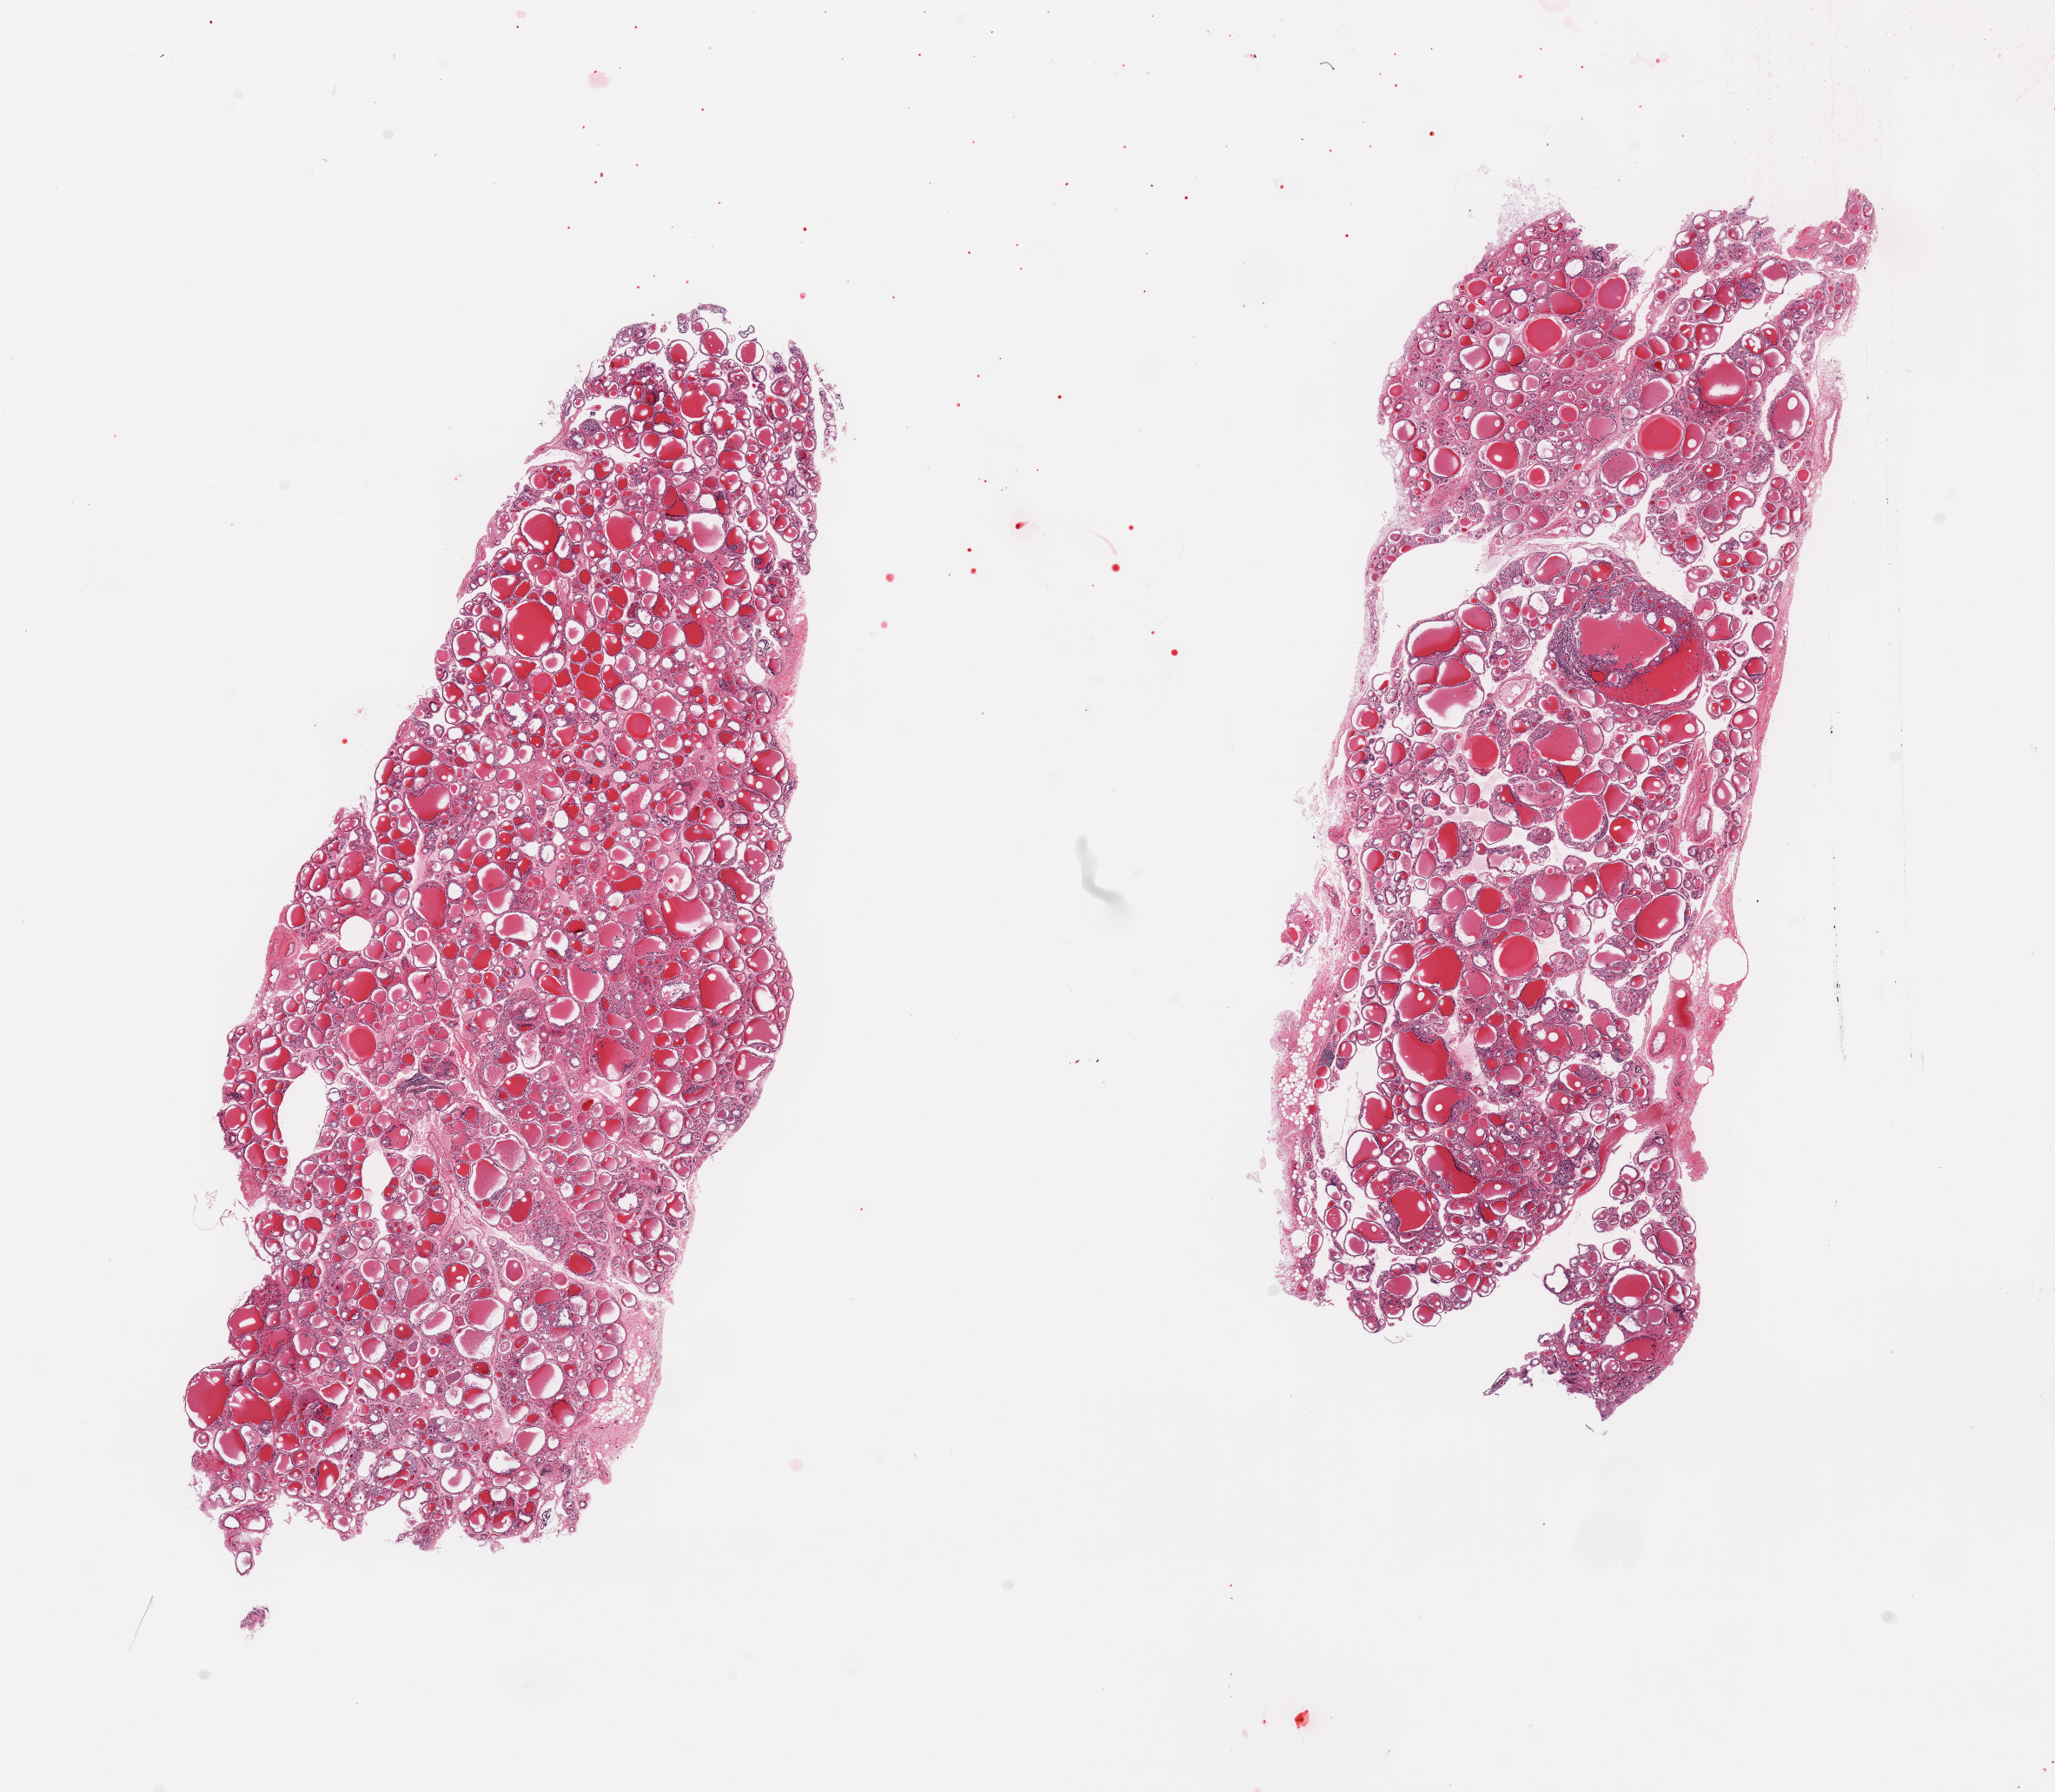
Whole-slide image, H&E stain — a low-resolution overview of the entire scanned area, about 18.7 x 16.3 mm, PAXgene-fixed paraffin-embedded (PFPE) section, target tissue: thyroid, tissue donor sample. Male donor.
- review note (as recorded): 2 pieces, microndular goitre, degenerative/regressive changes